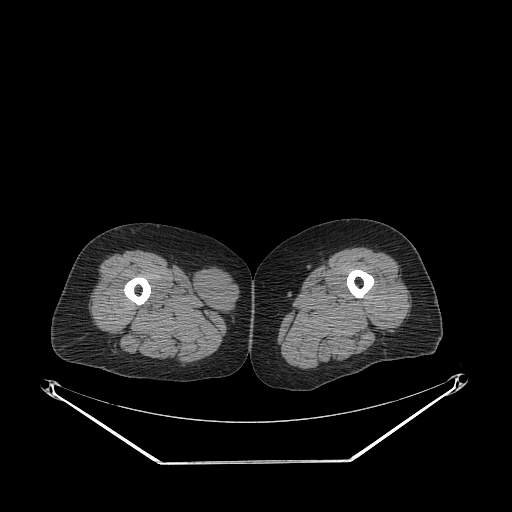
CT of an extremity soft-tissue mass (from a PET/CT study), one axial slice. Position 237 of 311 along the scan axis. Reconstruction kernel STANDARD. 140 kVp. Soft-tissue window (W 400 / L 40 HU). 512 × 512 image matrix, field of view 500 × 500 mm. Female patient. Case-level facts recorded for this patient, not image findings: histological type: leiomyosarcoma; grade: intermediate; site of the primary tumour: parascapusular.
Annotated regions visible in this slice (expert contour drawn on MRI and transferred to this co-registered scan by the dataset authors):
- gross tumour volume including surrounding oedema: bounding box [x1, y1, x2, y2] px = [194, 267, 241, 316]
- gross tumour volume (mass): [194, 267, 241, 316]